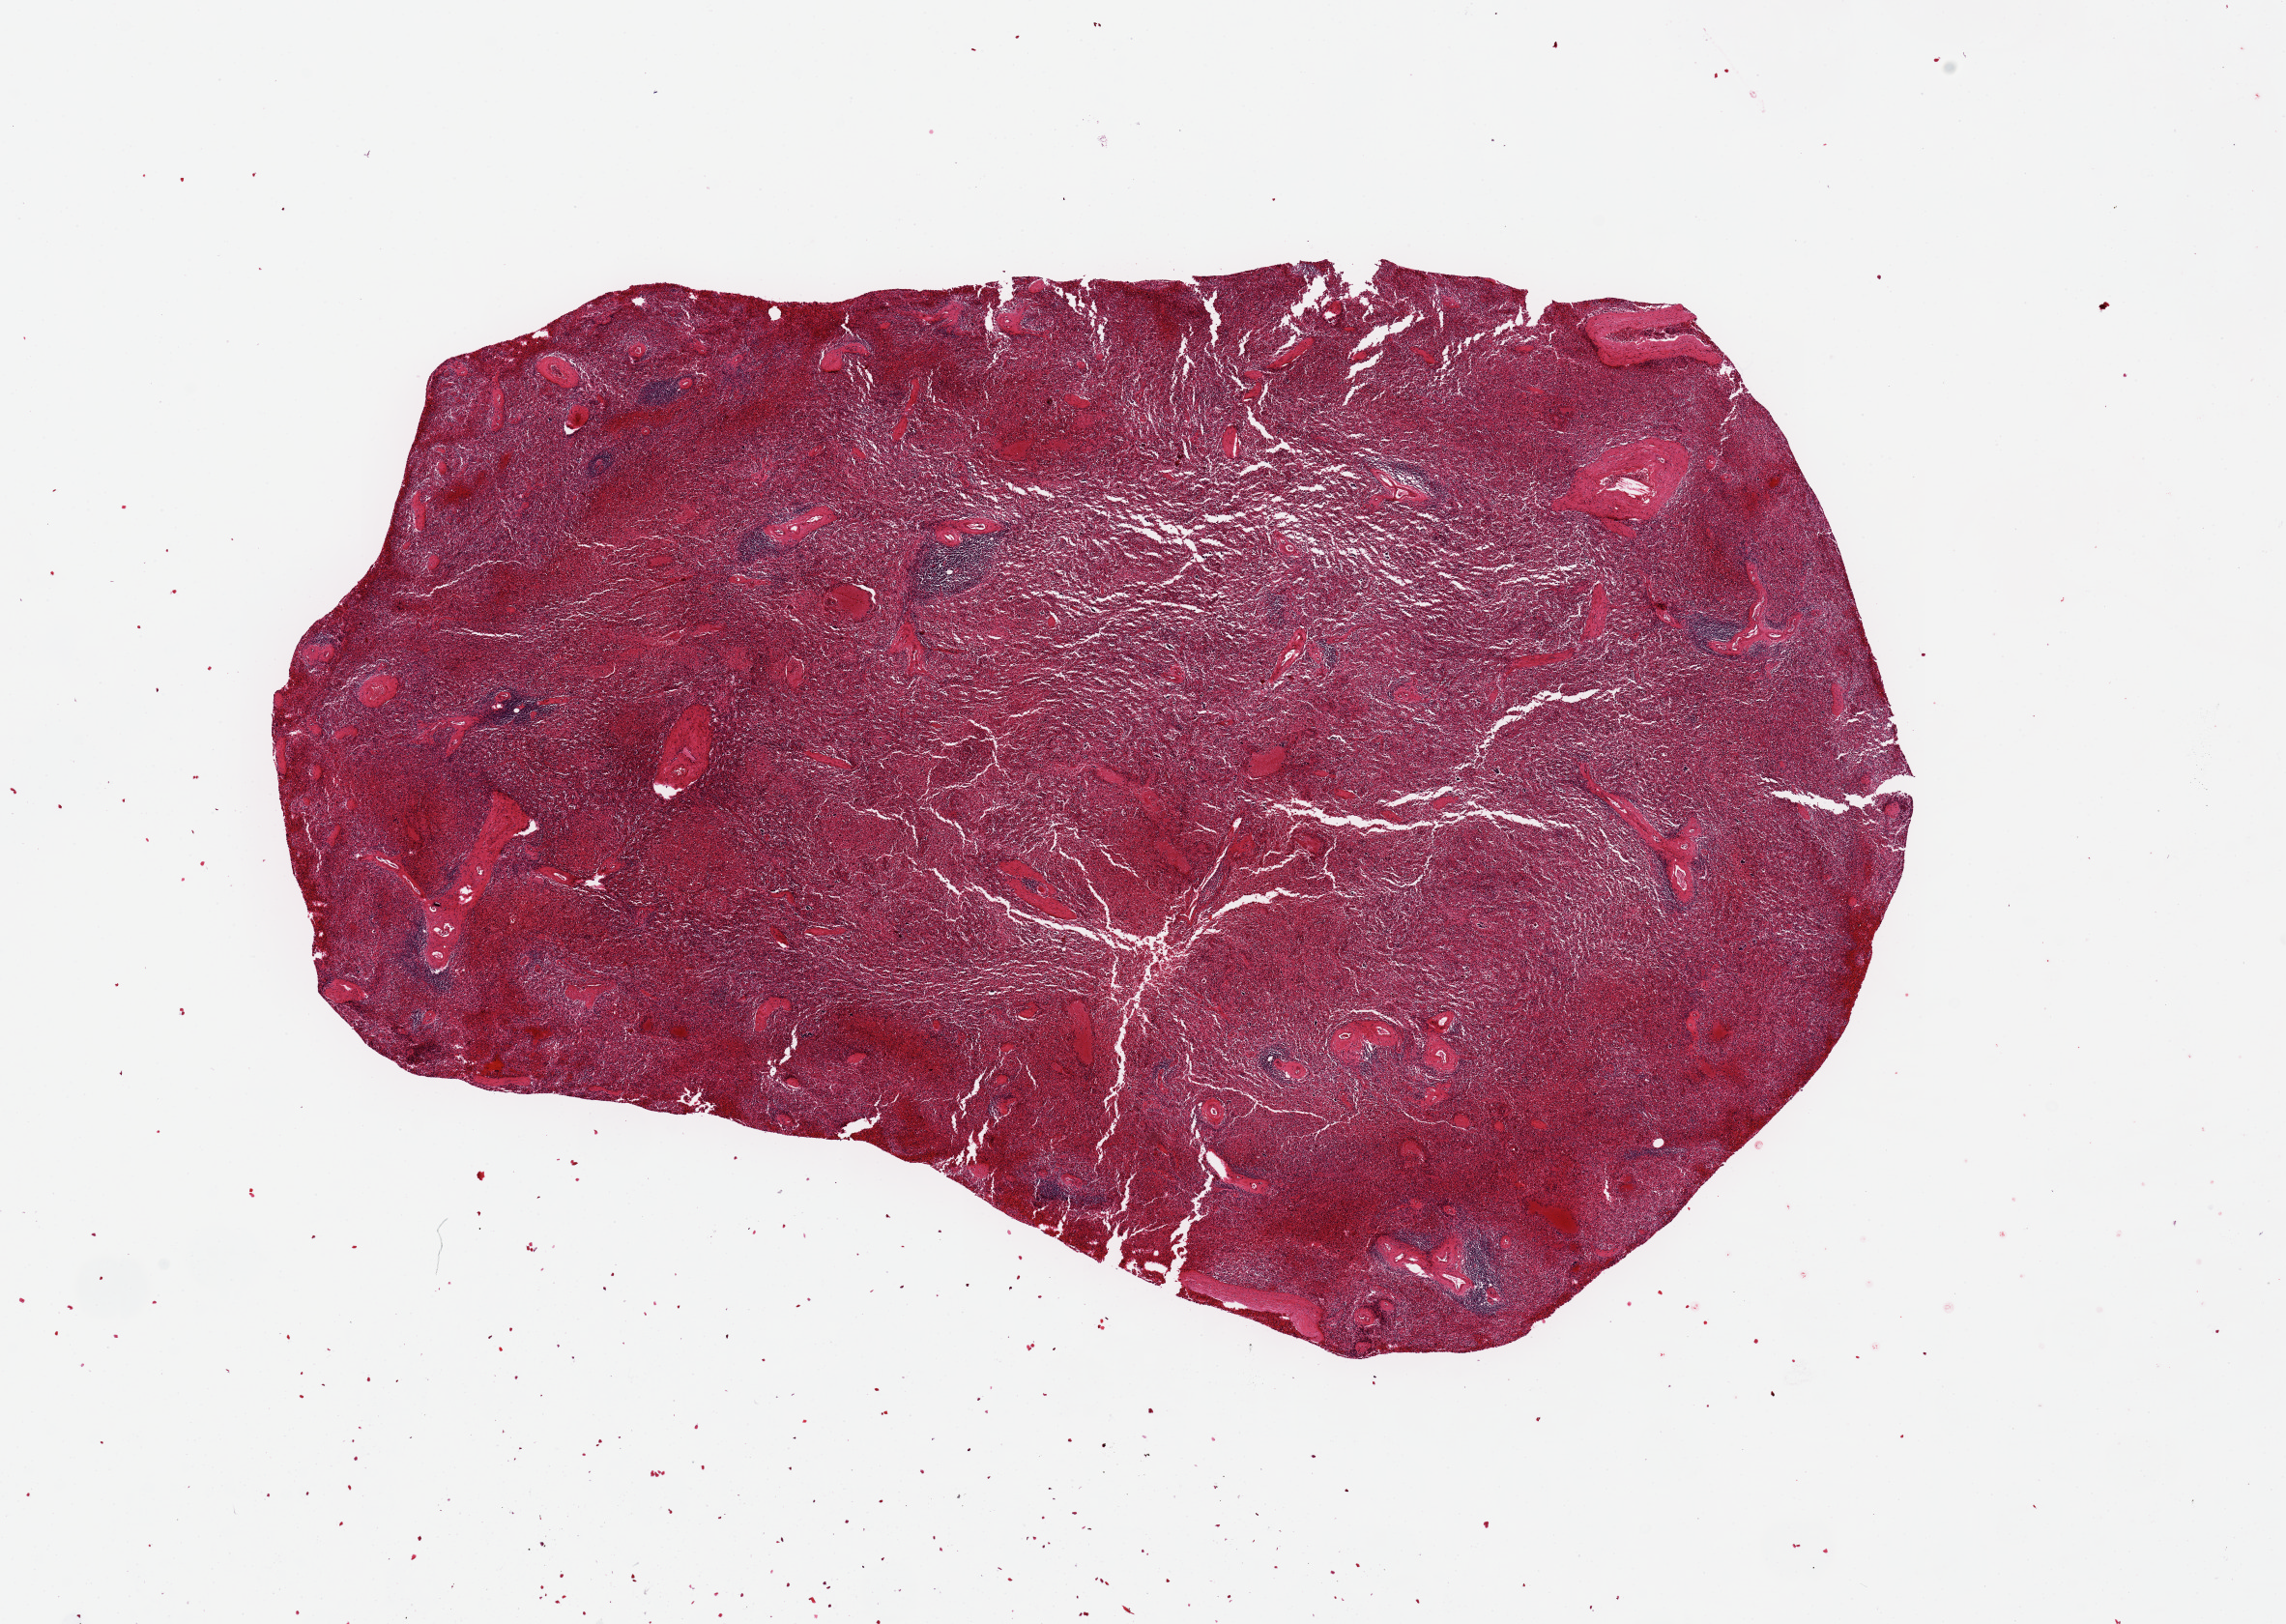
Haematoxylin and eosin whole-slide image, brightfield, a low-resolution overview of the entire scanned area, about 18.7 x 13.3 mm; PAXgene-fixed, paraffin-embedded tissue; section of spleen (target tissue); tissue donor sample. Female donor.
- pathologist's review note for this sample: 13x8 mm; moderate congestion